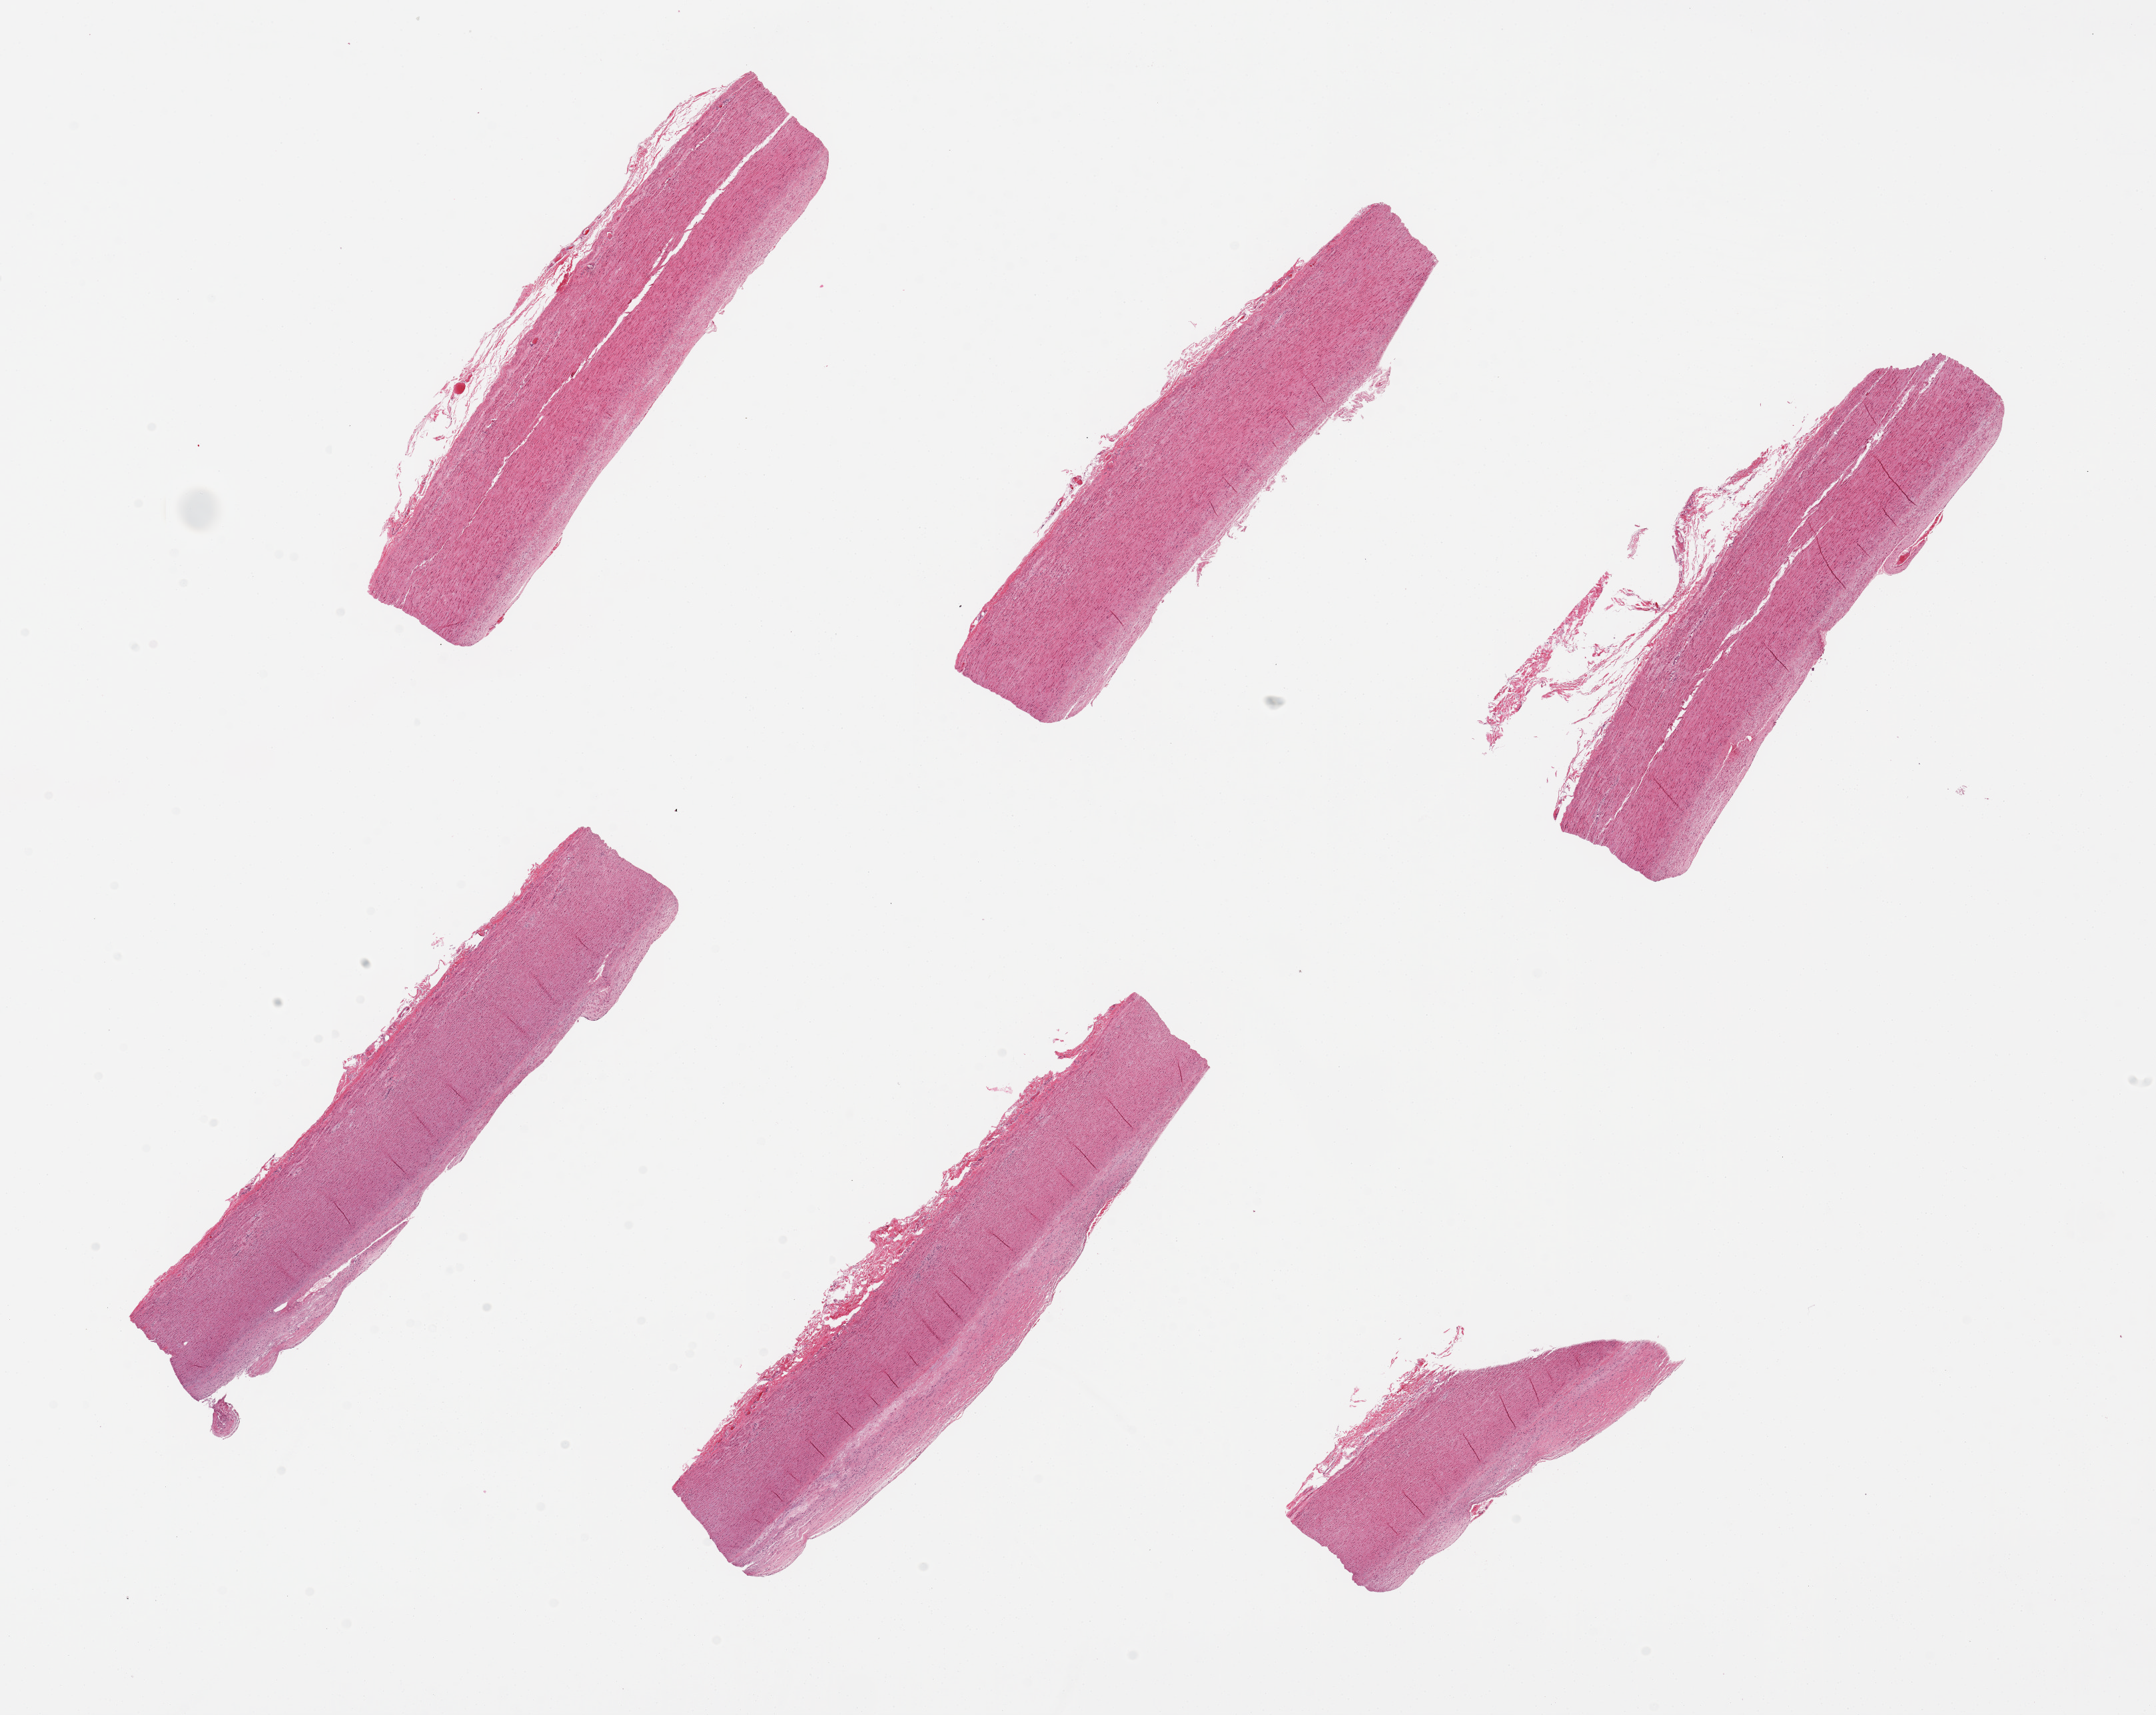
Whole-slide image, haematoxylin and eosin stain, a low-resolution overview of the entire scanned area, about 25.6 x 20.4 mm, PAXgene-fixed paraffin-embedded (PFPE) section, target tissue: aorta, donor tissue sample. Donor: male.
• review note (as recorded): 6 pieces. up to 8x2mm